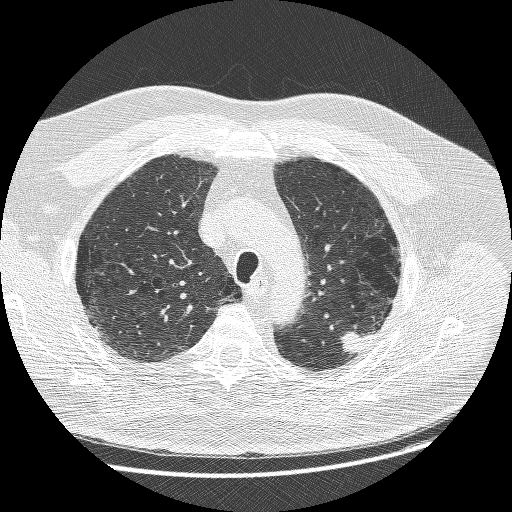
Low-dose screening chest CT, axial slice. Baseline screening round. Lung window (W 1500 / L -600 HU). 1.25 mm slice thickness. Lung (sharp) reconstruction kernel (BONE). Slice 203 of 258 in the series. Male, age 68 years at enrolment.
Expert reader's lesion annotation, bounding box <331,319,388,364> (left, top, right, bottom; pixels). Screening reader's record for this exam (one nodule recorded; not confirmed to be the boxed lesion): non-calcified nodule or mass ≥4 mm, left upper lobe, 15 × 14 mm, smooth margins, soft tissue attenuation. Participant outcome: lung cancer diagnosed 19 days after this screen — adenosquamous carcinoma, left upper lobe, poorly differentiated (G3), stage IIIB (AJCC 6th edition), 32 mm at pathology.